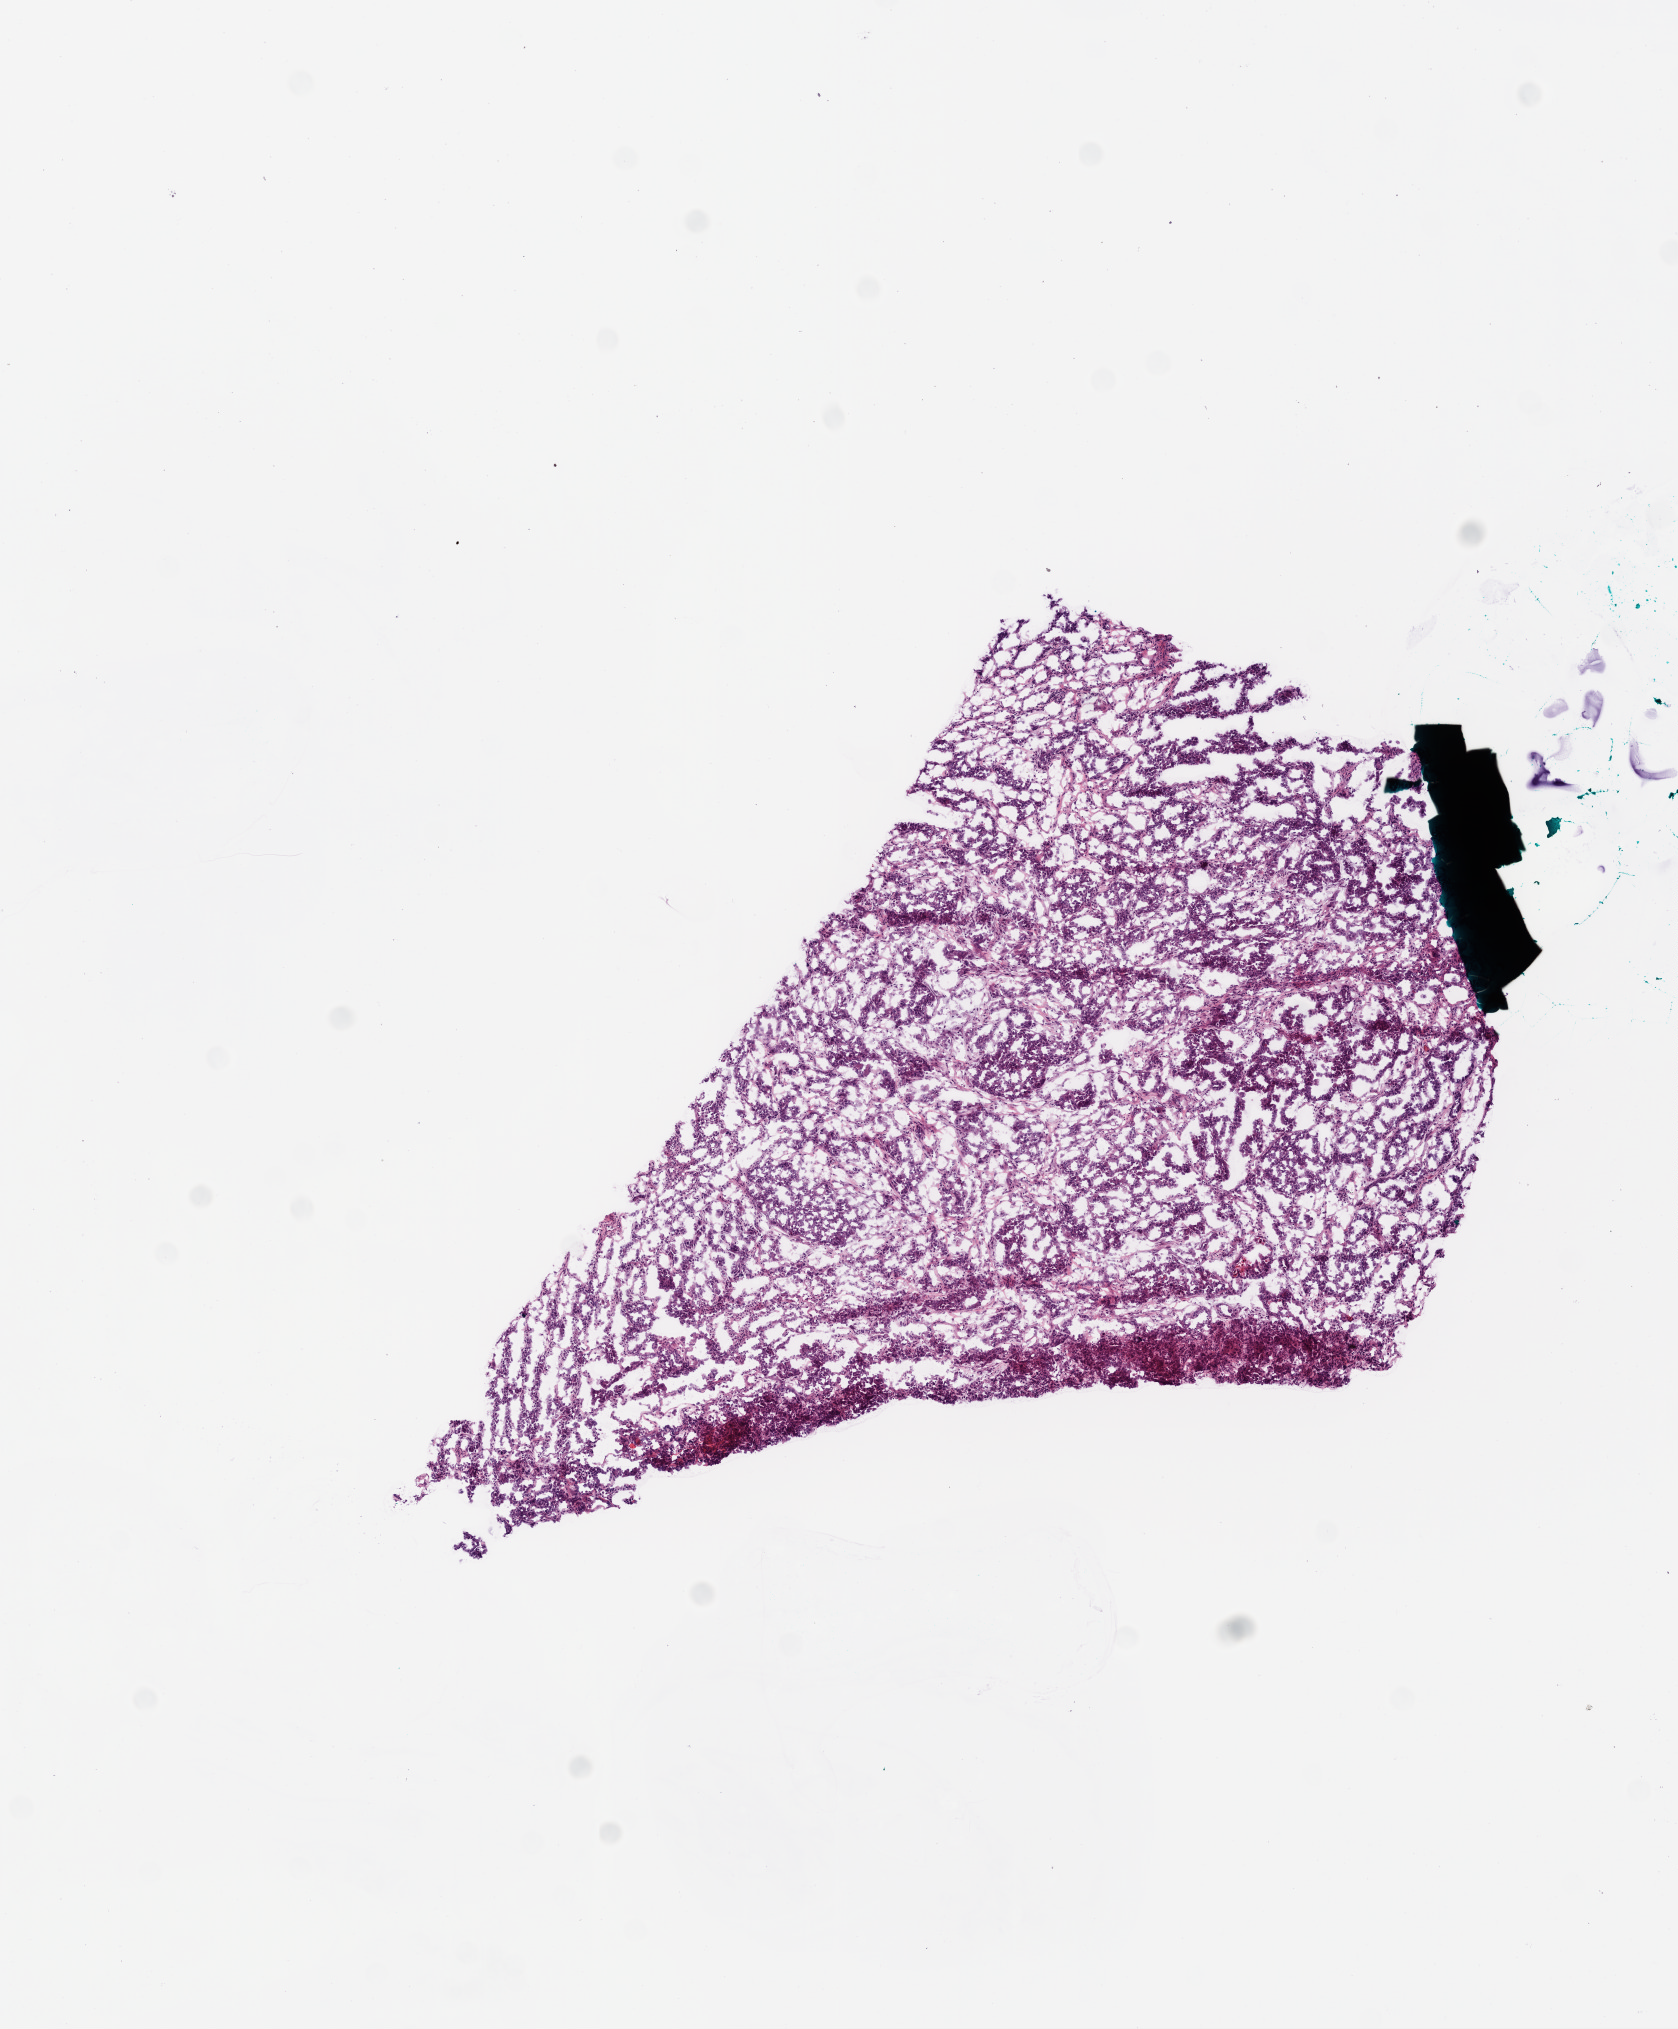
Whole-slide histology image, H&E — shown as a low-resolution overview of the whole scanned area (about 6.8 x 8.2 mm, acquisition: 20x scan). Frozen section. Sample: primary tumour, ovary. Female patient; age at initial diagnosis 59 years. Pathologist review of this section (percent, as recorded): tumour cells 80%, tumour nuclei 85%.
Histologic diagnosis: Serous cystadenocarcinoma, NOS.